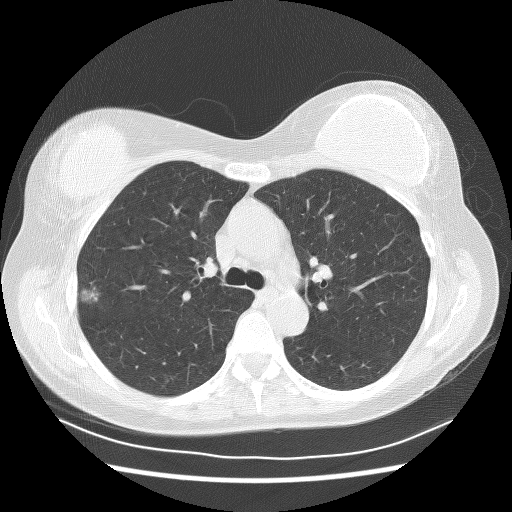
Low-dose screening chest CT, axial slice. Baseline screening round. Lung window (W 1500 / L -600 HU). 2.5 mm slice thickness. Slice 79 of 253 in the series. 512 × 512 image matrix. Female participant, aged 58 years at enrolment. Former smoker at enrolment.
• Expert reader's lesion annotation, box from (x=66, y=272) to (x=111, y=312) px.
• The screening reader recorded 2 non-calcified nodules or masses ≥4 mm on this exam (right upper lobe, right upper lobe); which of them this box marks is not recorded.
• Official screen result: positive, change unspecified: nodule(s) >= 4 mm or enlarging nodule(s), mass(es), or other non-specific abnormalities suspicious for lung cancer.
• Lung cancer was diagnosed 510 days after this screen: bronchiolo-alveolar adenocarcinoma, NOS, right upper lobe, well differentiated (G1), stage IA (AJCC 6th edition).